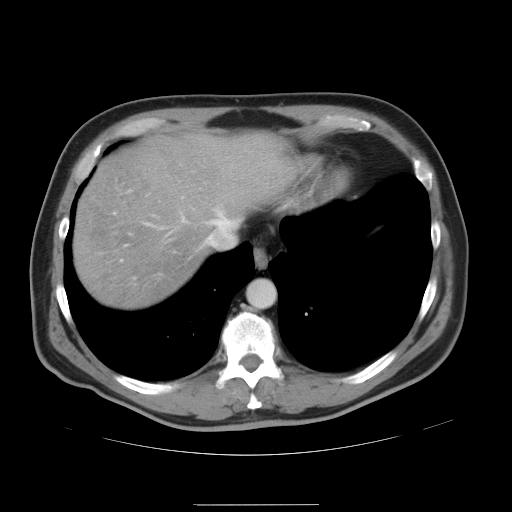
Contrast-enhanced abdominal CT, one axial slice. Position 41 of 47 along the scan axis. Soft-tissue window (W 400 / L 40 HU). 512 × 512 image matrix, field of view 420 × 420 mm. Male patient, age 61 years. Case-level facts recorded for this patient, not image findings: diagnosis: colorectal cancer liver metastases, imaged before liver resection; multiple liver metastases: no; largest metastasis: 1.2 cm; disease in both lobes: no.
Annotated regions visible in this slice (expert manual segmentation):
- hepatic veins: bounding box [x1, y1, x2, y2] px = [161, 207, 239, 247]
- liver: [74, 133, 298, 309]
- planned liver remnant (the part of the liver to remain after resection): [74, 133, 298, 309]